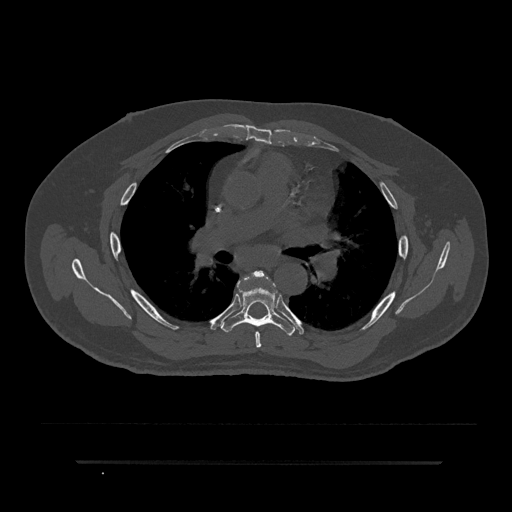
CT including the spine, one axial slice; 120 kVp; bone window (W 1800 / L 400 HU); 0.5 mm slice thickness; 512 × 512 image matrix, field of view 464 × 464 mm. Male patient, age 59 years. Case-level facts recorded for this patient, not image findings: primary cancer: bile ducts; vertebrae with lytic lesions (as recorded): T10.
Structures marked on this image (semi-automatic segmentation, software-assisted and operator-edited):
- T5 vertebra: bounding box (x1, y1, x2, y2) in pixels: (247, 271, 265, 348)
- T6 vertebra: (221, 286, 294, 336)